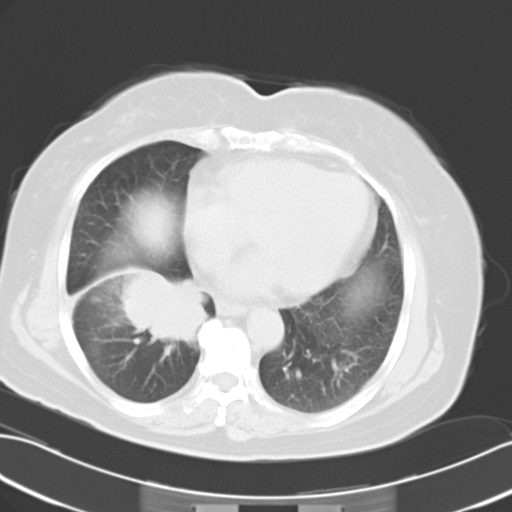
Chest CT, one axial slice; reconstruction kernel B40f; lung window (W 1500 / L -600 HU); 10 mm slice thickness; 512 × 512 image matrix, field of view 353 × 353 mm. Female patient, age 63 years. Case-level facts recorded for this patient, not image findings: clinical TNM (as recorded): T3 N0 M0.
Structures marked on this image (rectangle marked by the reading radiologist):
- lung tumour (recorded histology: adenocarcinoma): bounding box (x1, y1, x2, y2) in pixels: (122, 271, 208, 350)